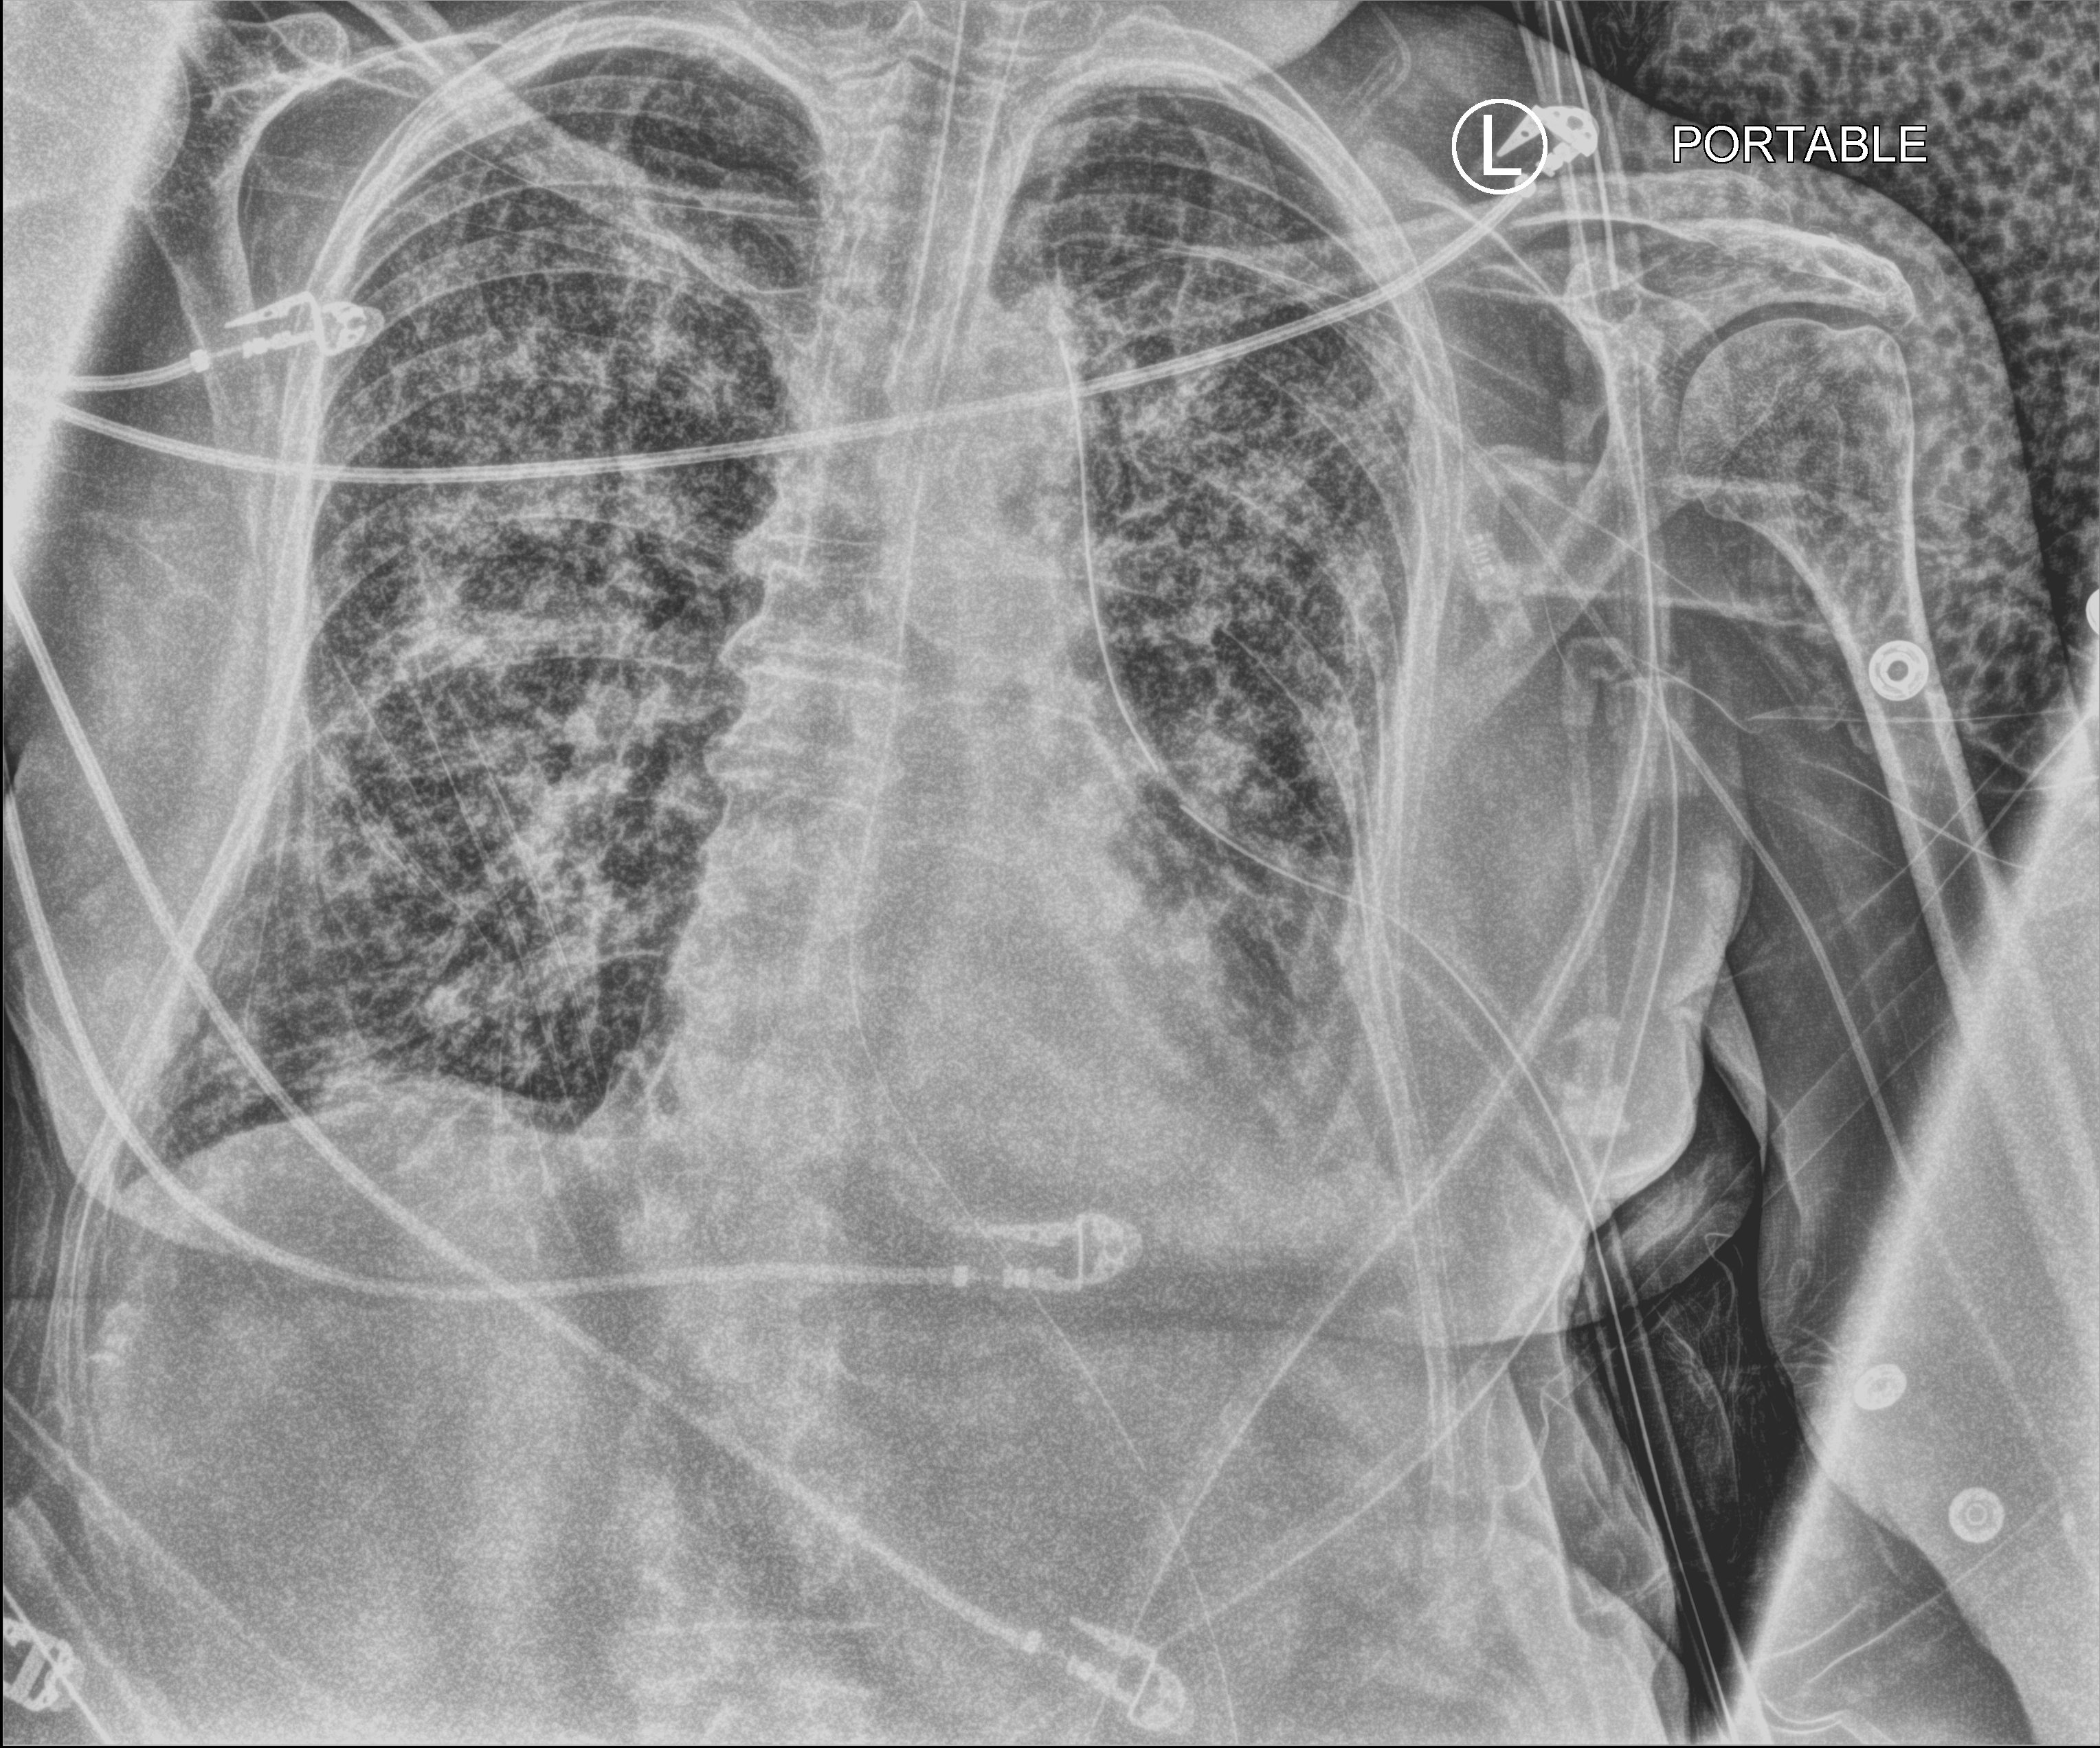
Portable chest radiograph. Female patient hospitalised with COVID-19, age 75–90 years.
Admission-level facts for this patient (not findings on this image; timing relative to this image not recorded): length of hospital stay: 70 days; admitted to intensive care during this hospital stay: yes.